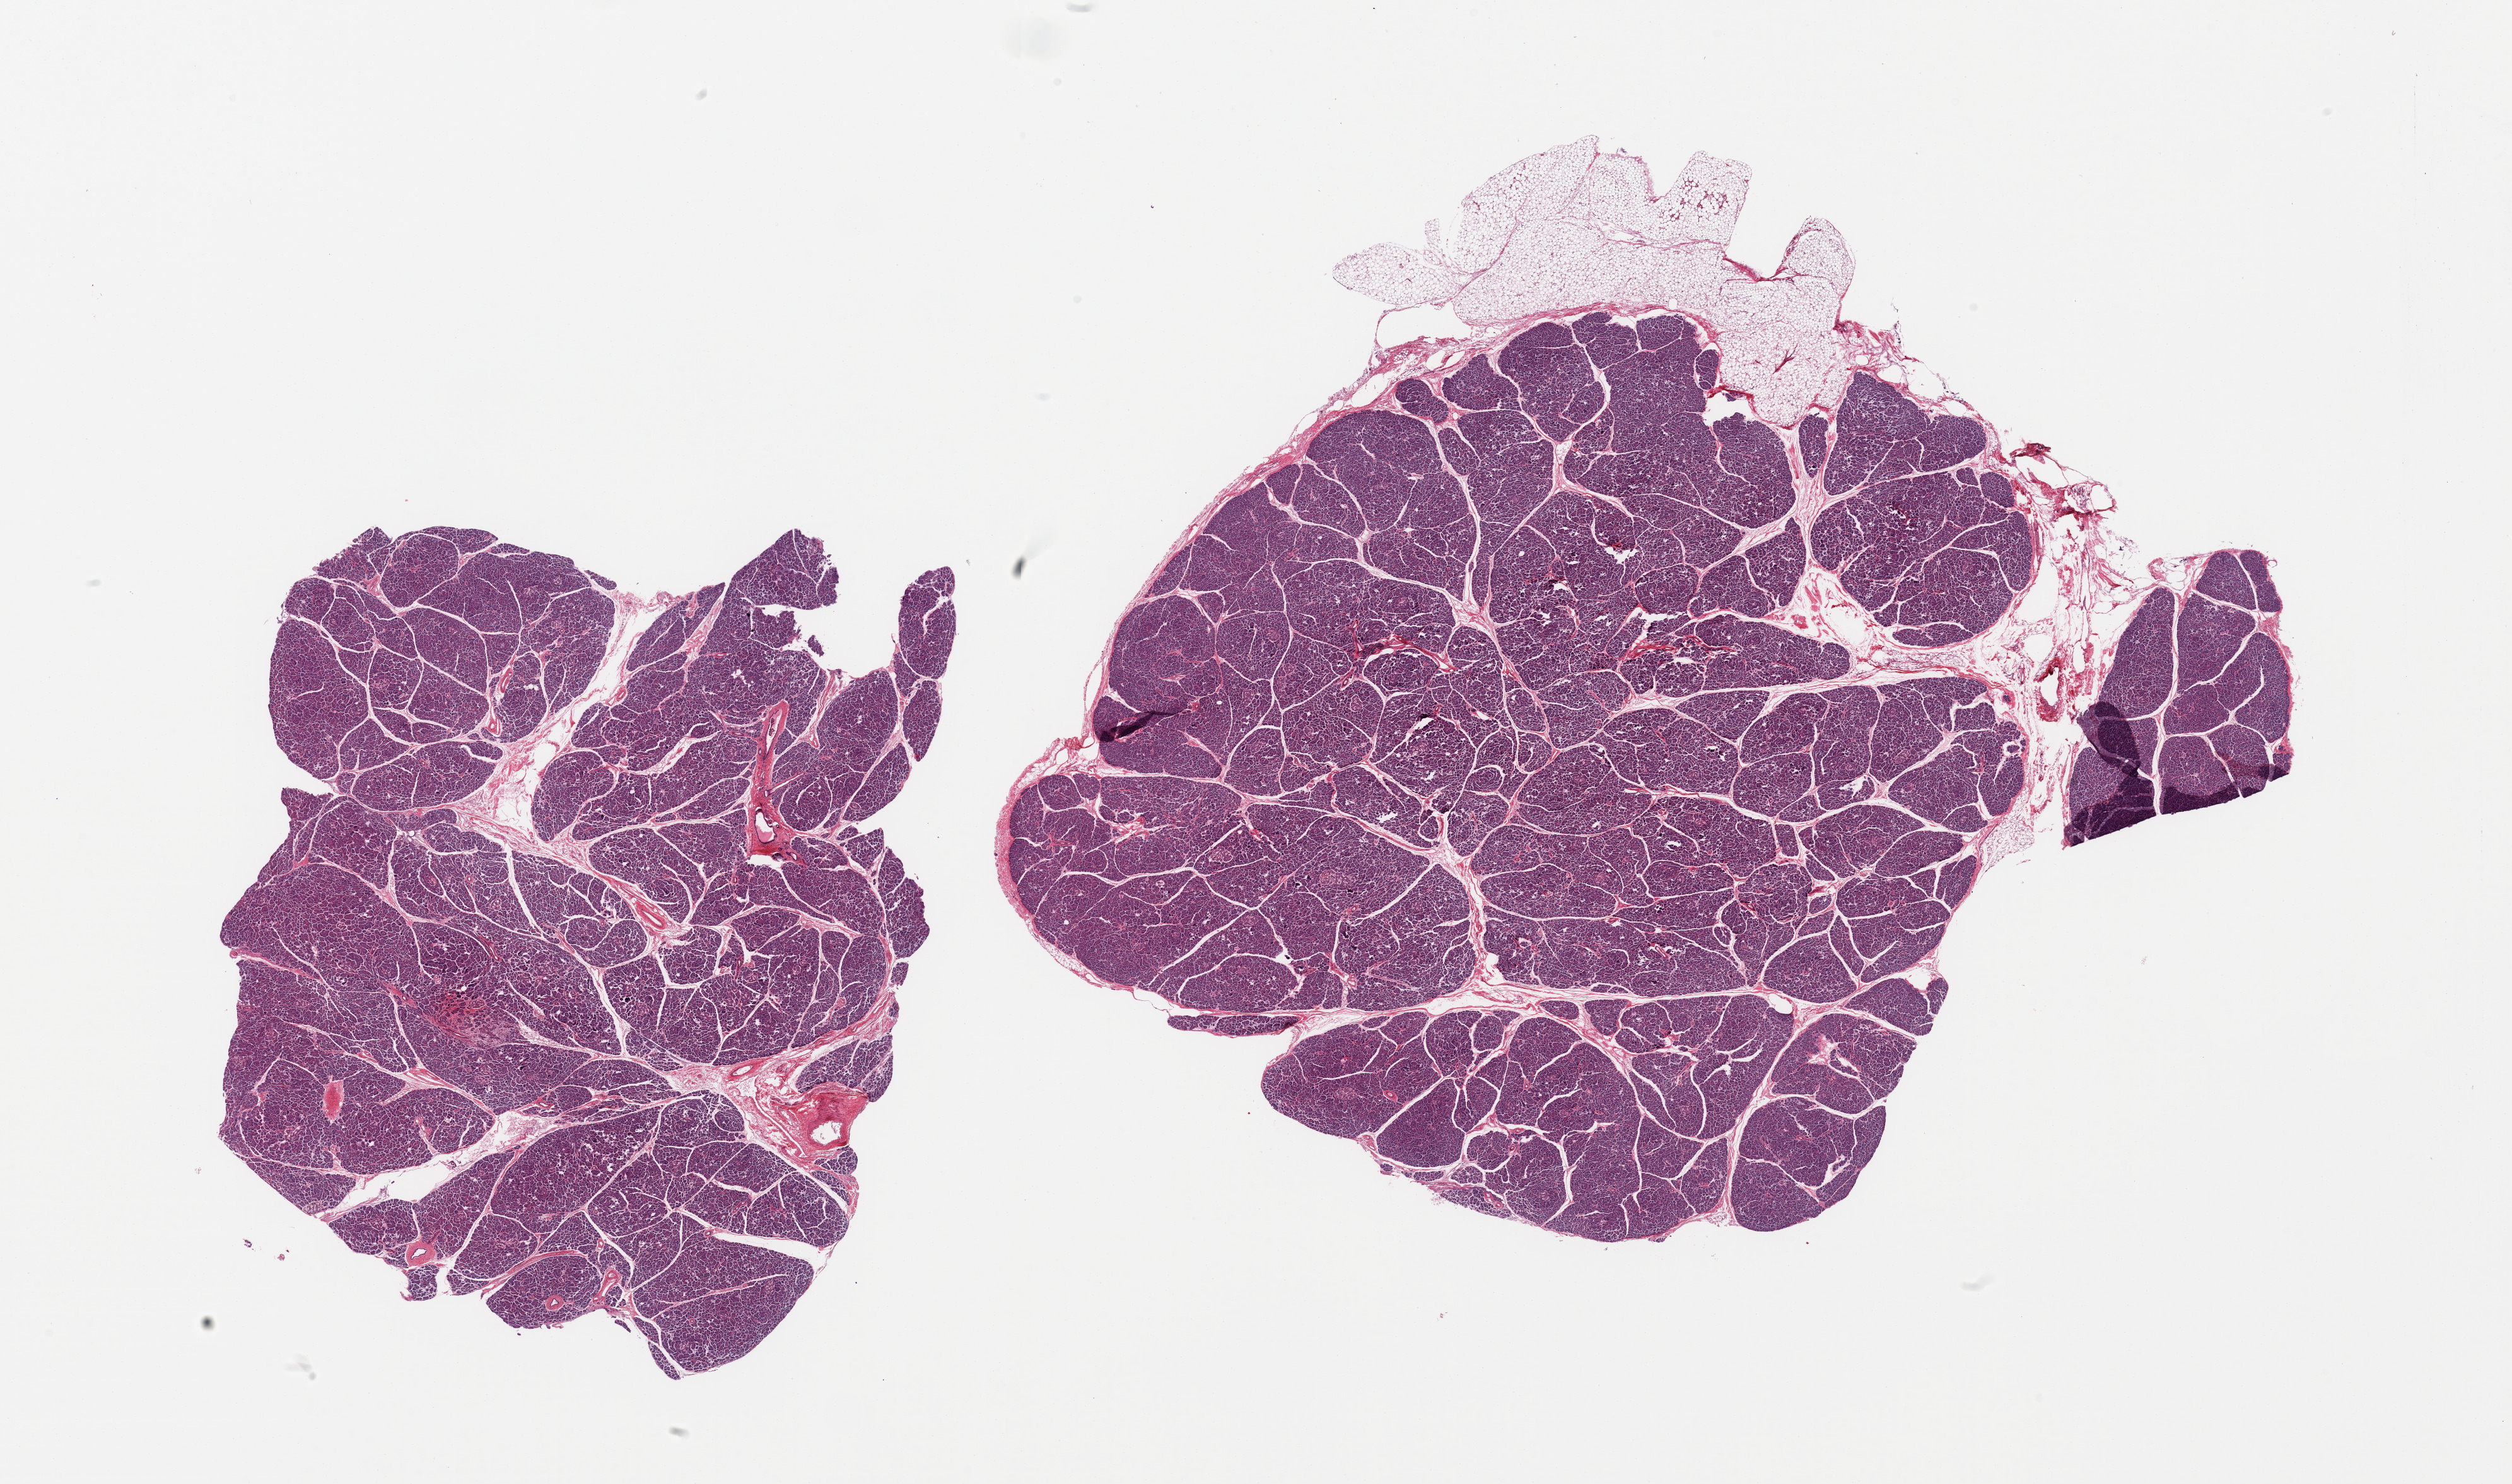
Digitized haematoxylin and eosin-stained section — low-resolution overview of the scanned area, about 31.5 x 18.6 mm (from a 20x scan), PAXgene-fixed, paraffin-embedded tissue, target tissue: pancreas, donor tissue sample. Donor: male.
Reviewer comment on this tissue sample: 2 pieces, well preserved, Islets abundant and well-visualized.